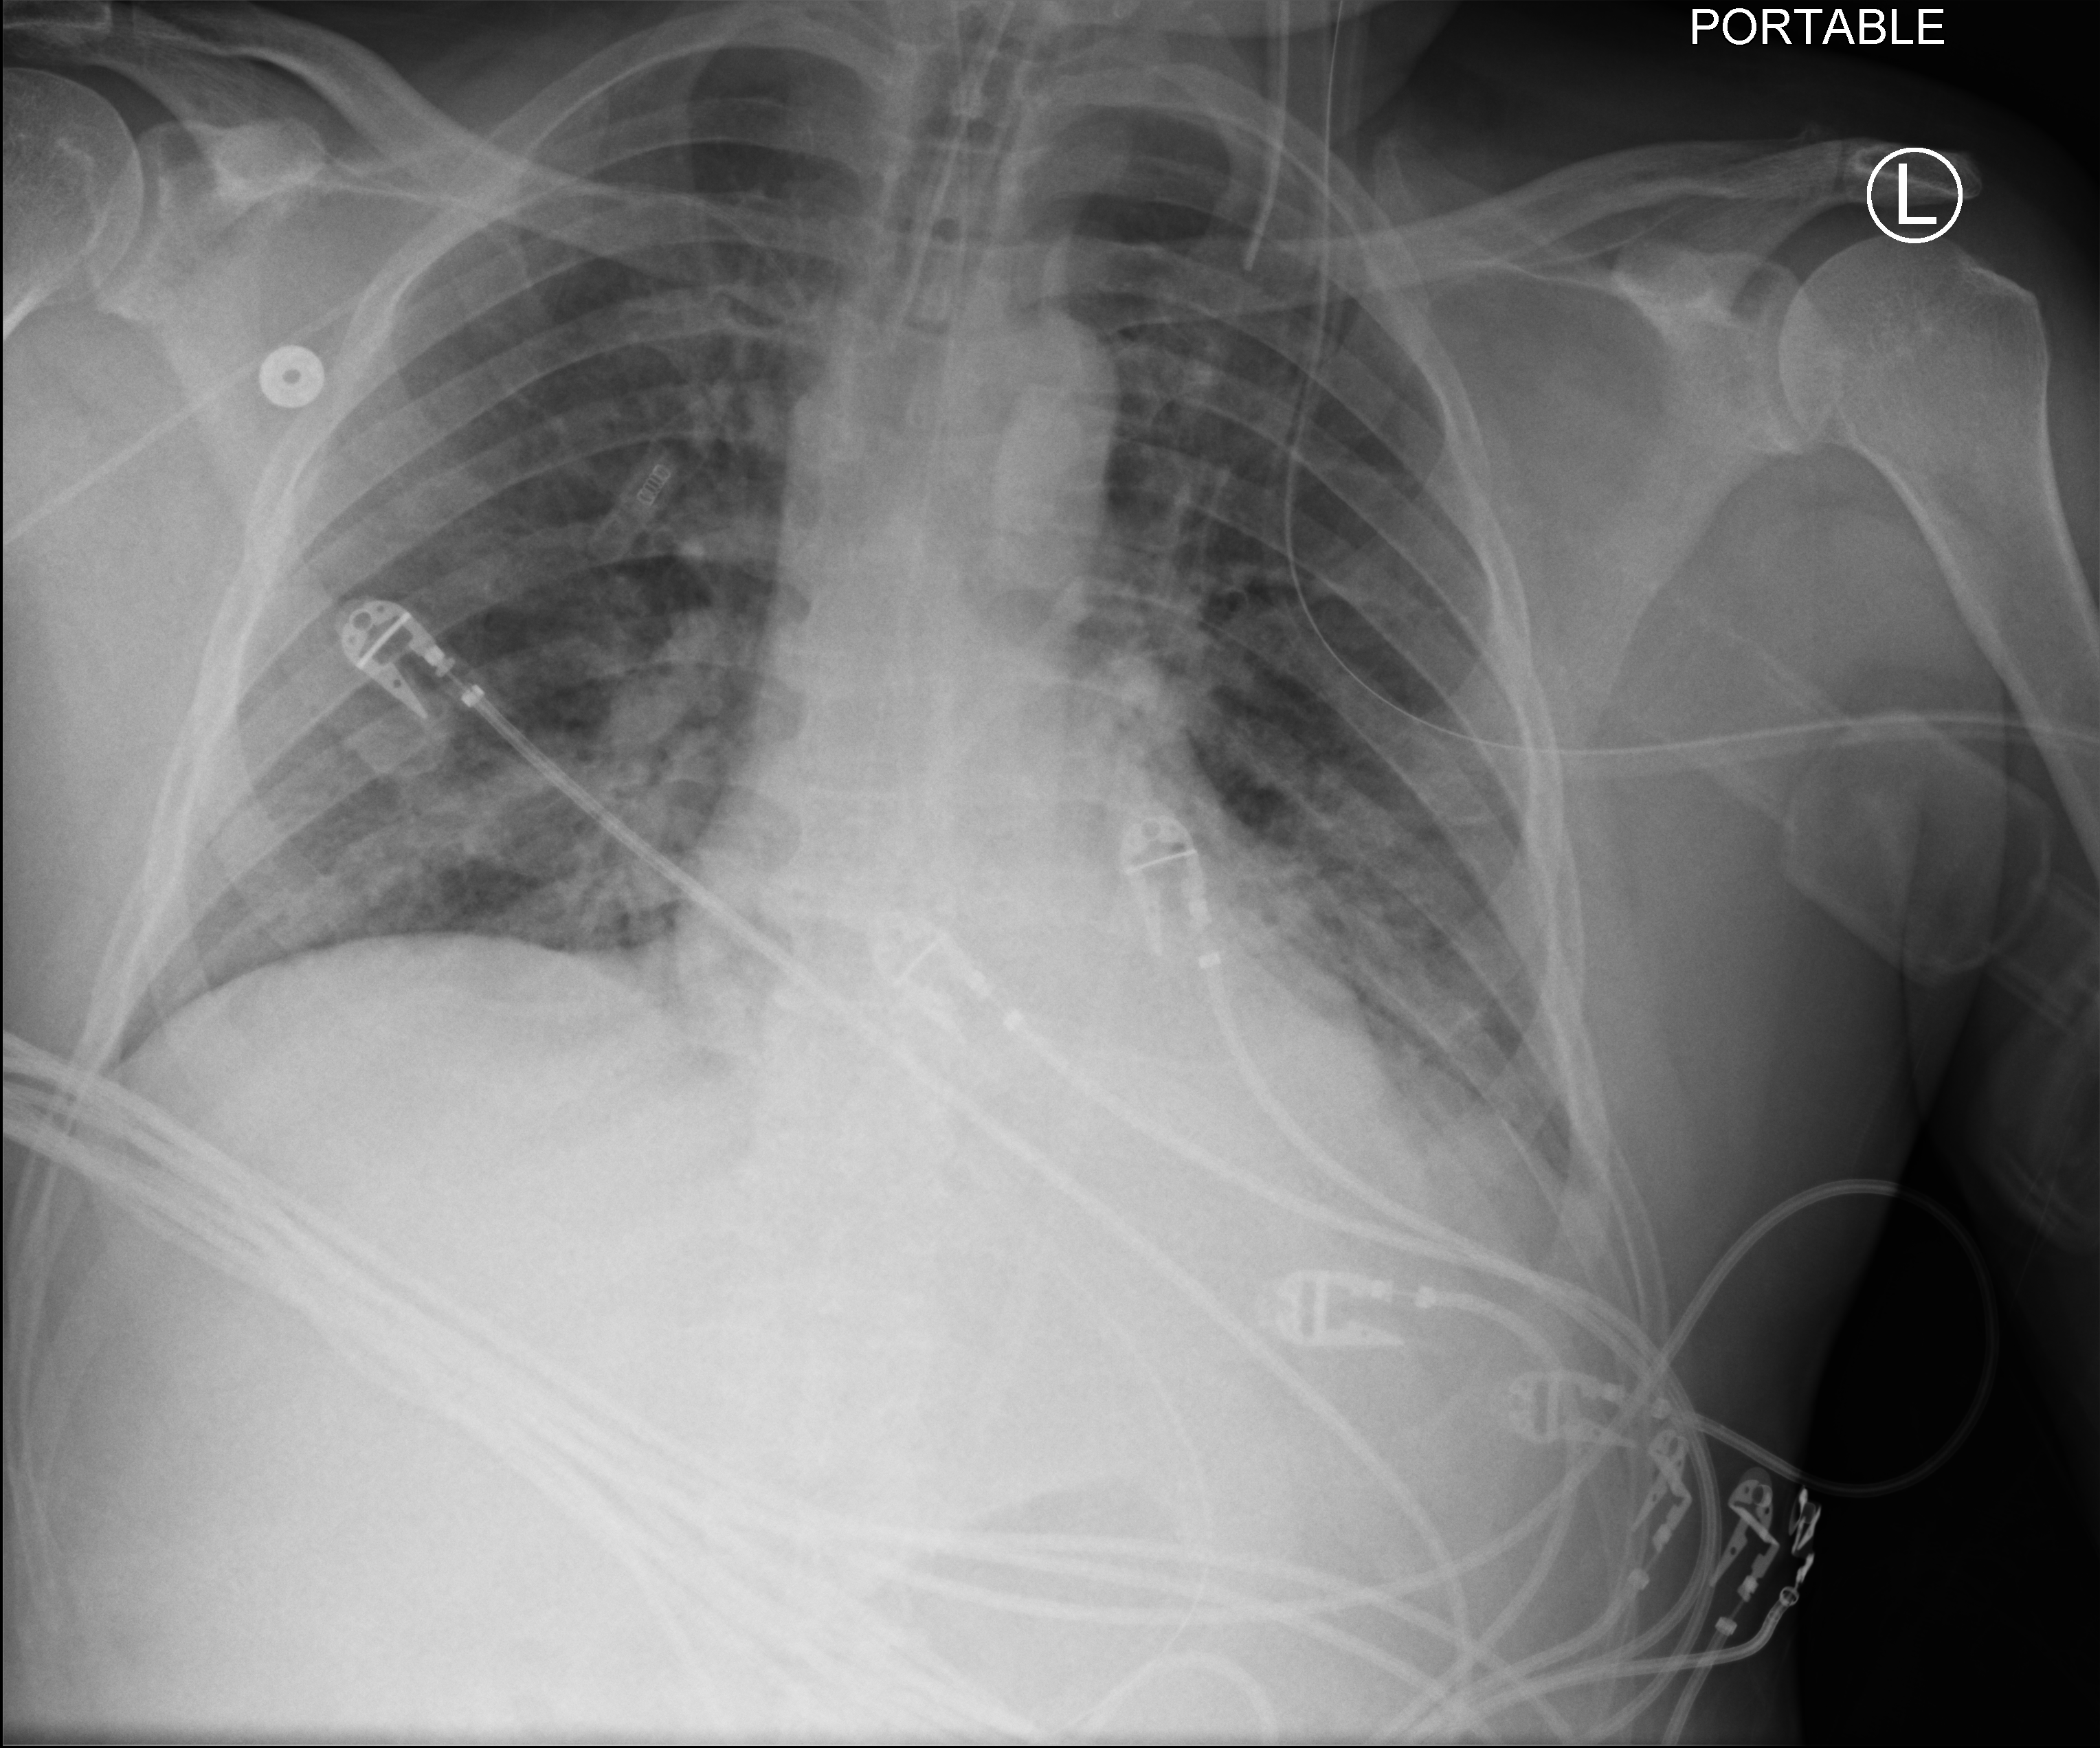
Chest X-ray (portable). Patient hospitalised with COVID-19; male, aged 18–59 years.
From the hospital-stay record, not from the radiograph (when in the stay this image was taken is not recorded): admitted to intensive care during this hospital stay: yes.